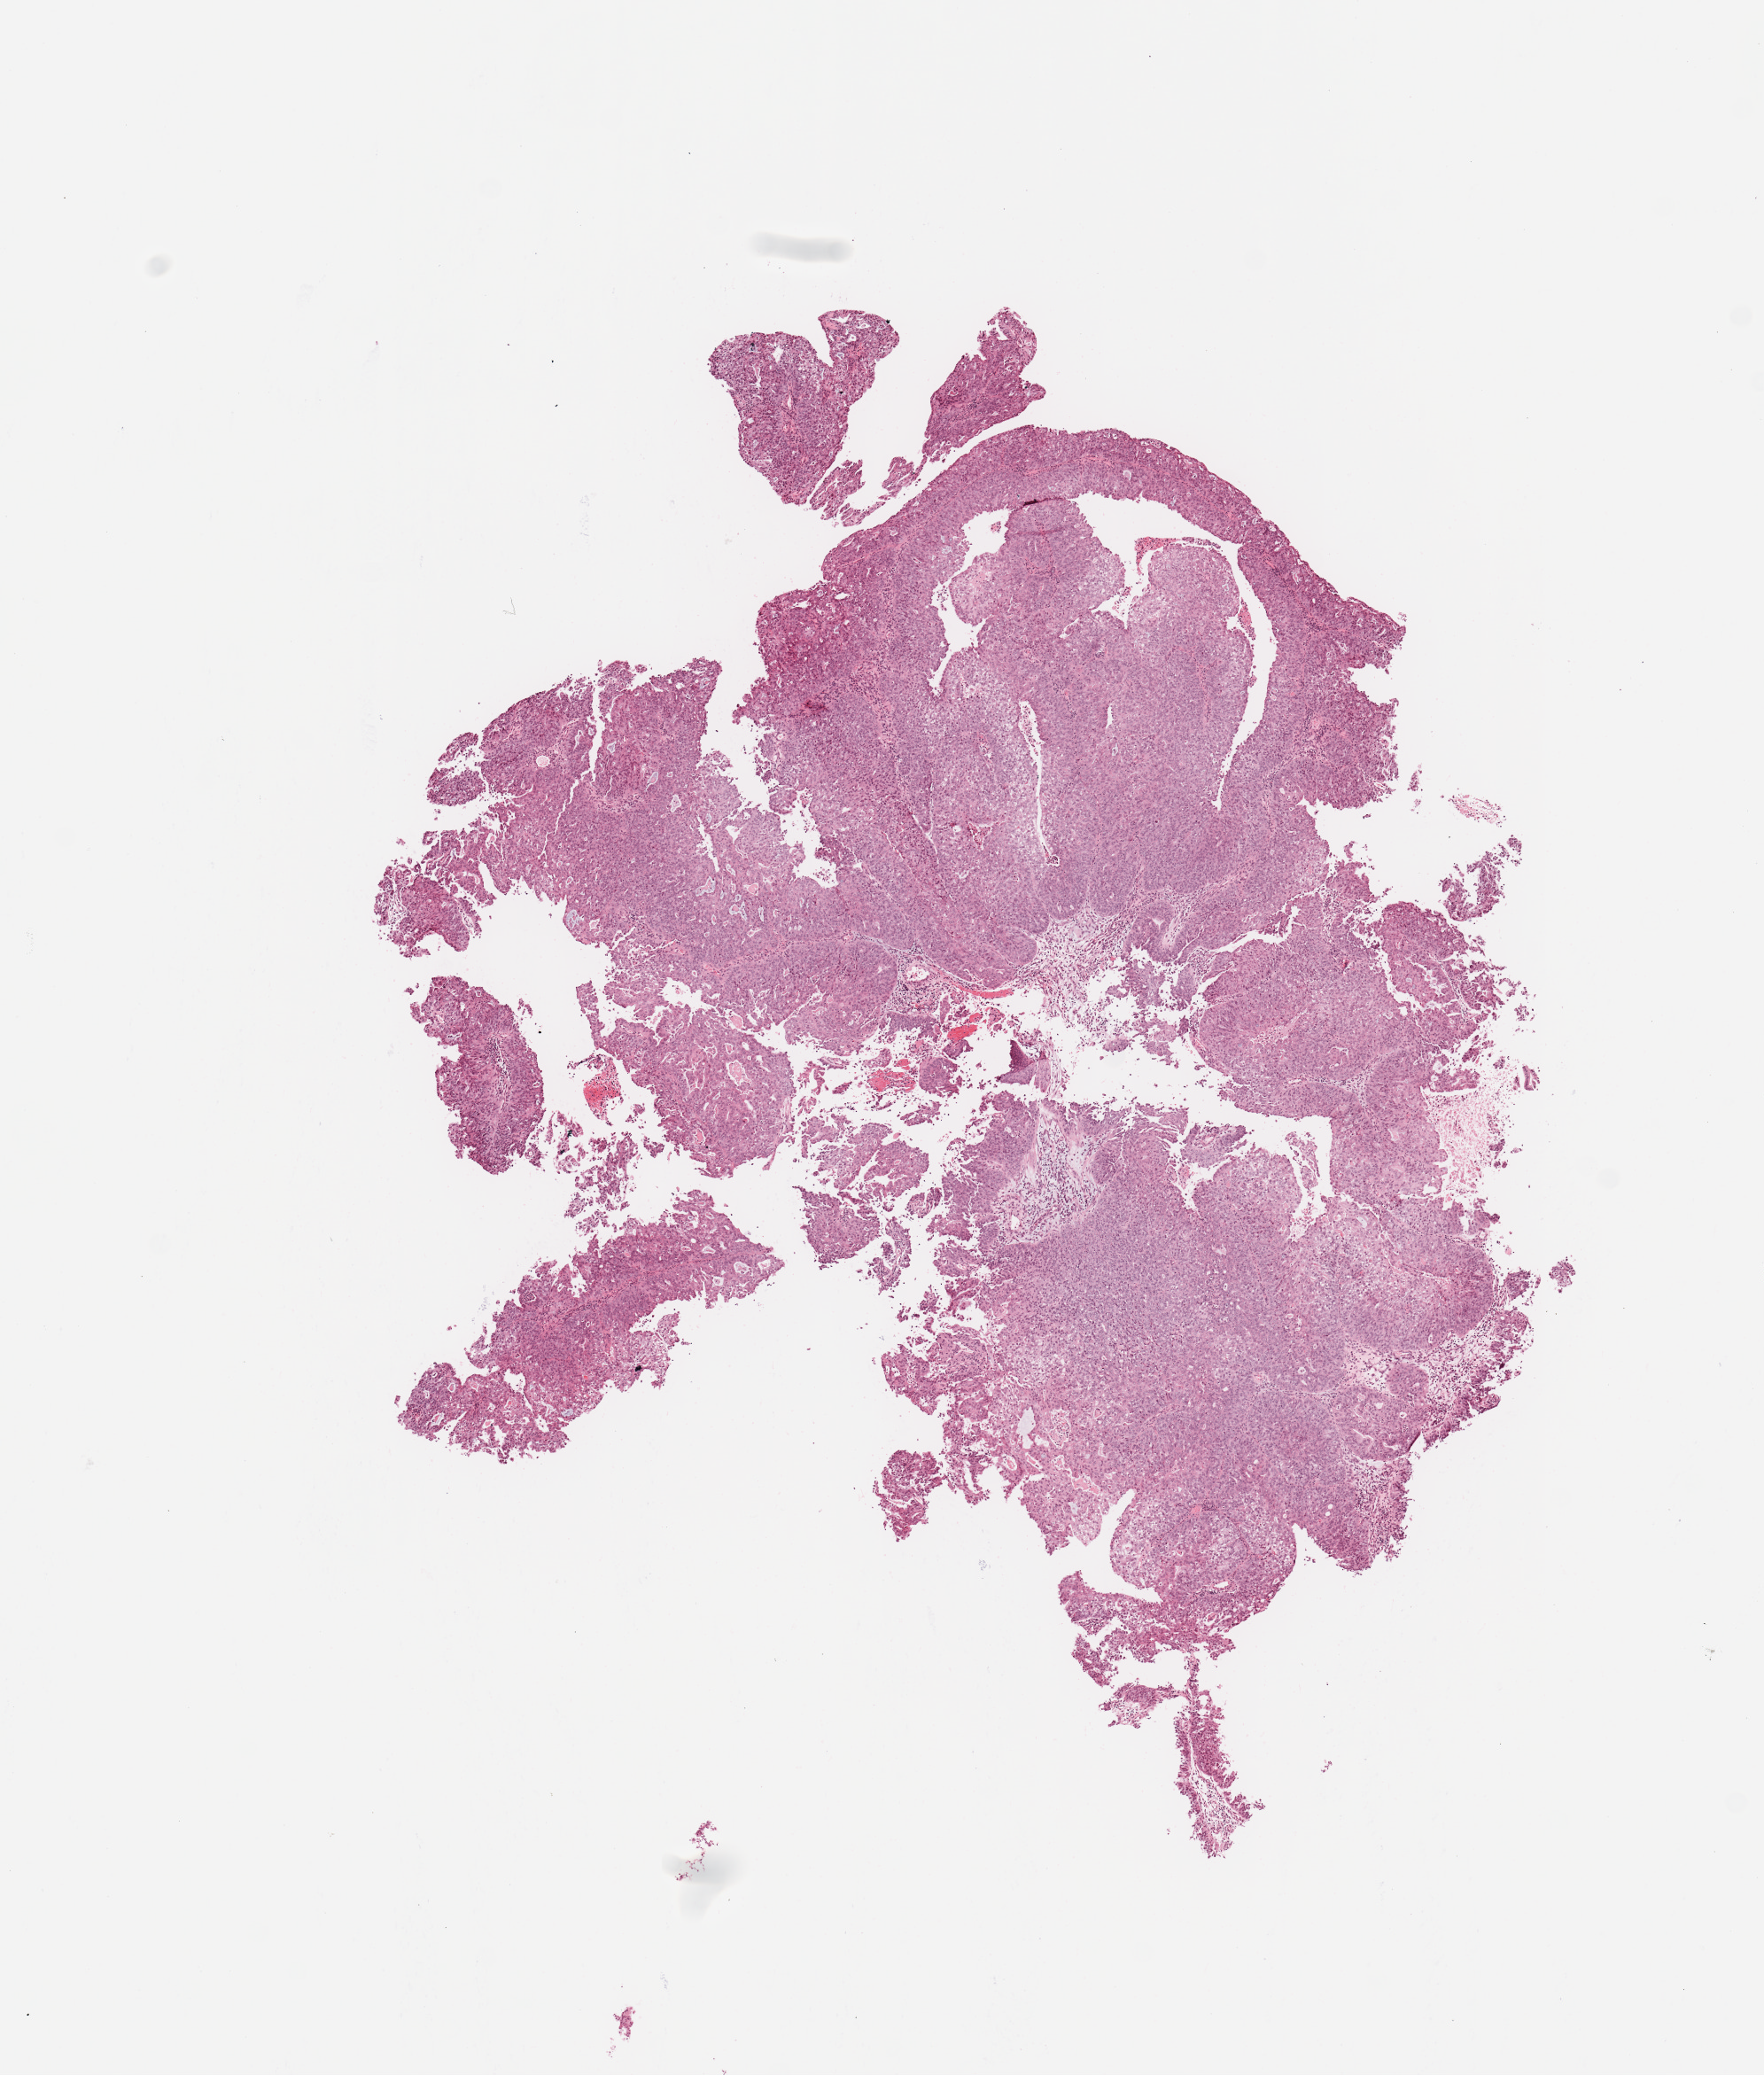
Whole-slide histology image, H&E — a low-resolution overview of the entire scanned area, about 7.9 x 9.3 mm, tumour tissue sample, sampled site: uterus. Female, 66 y/o. Histologic grade: G2 (moderately differentiated). Composition of this section per pathologist review: tumour nuclei 90%, necrosis 2%.
* diagnosis: Endometrioid adenocarcinoma, NOS
* AJCC pathologic stage: IB